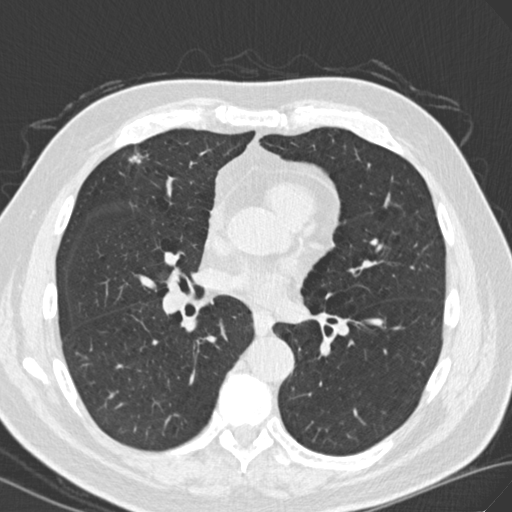
Low-dose screening chest CT, one axial slice. Slice 82 of 171 in the series (ordered by position). Reconstruction kernel B30f. 120 kVp. Lung window (W 1500 / L -600 HU). 512 × 512 image matrix.
Structures marked on this image (outlined manually by an expert reader):
- lesion 1 (tumor, upper lobe of right lung): bounding box [x1, y1, x2, y2] px = [129, 153, 142, 163]